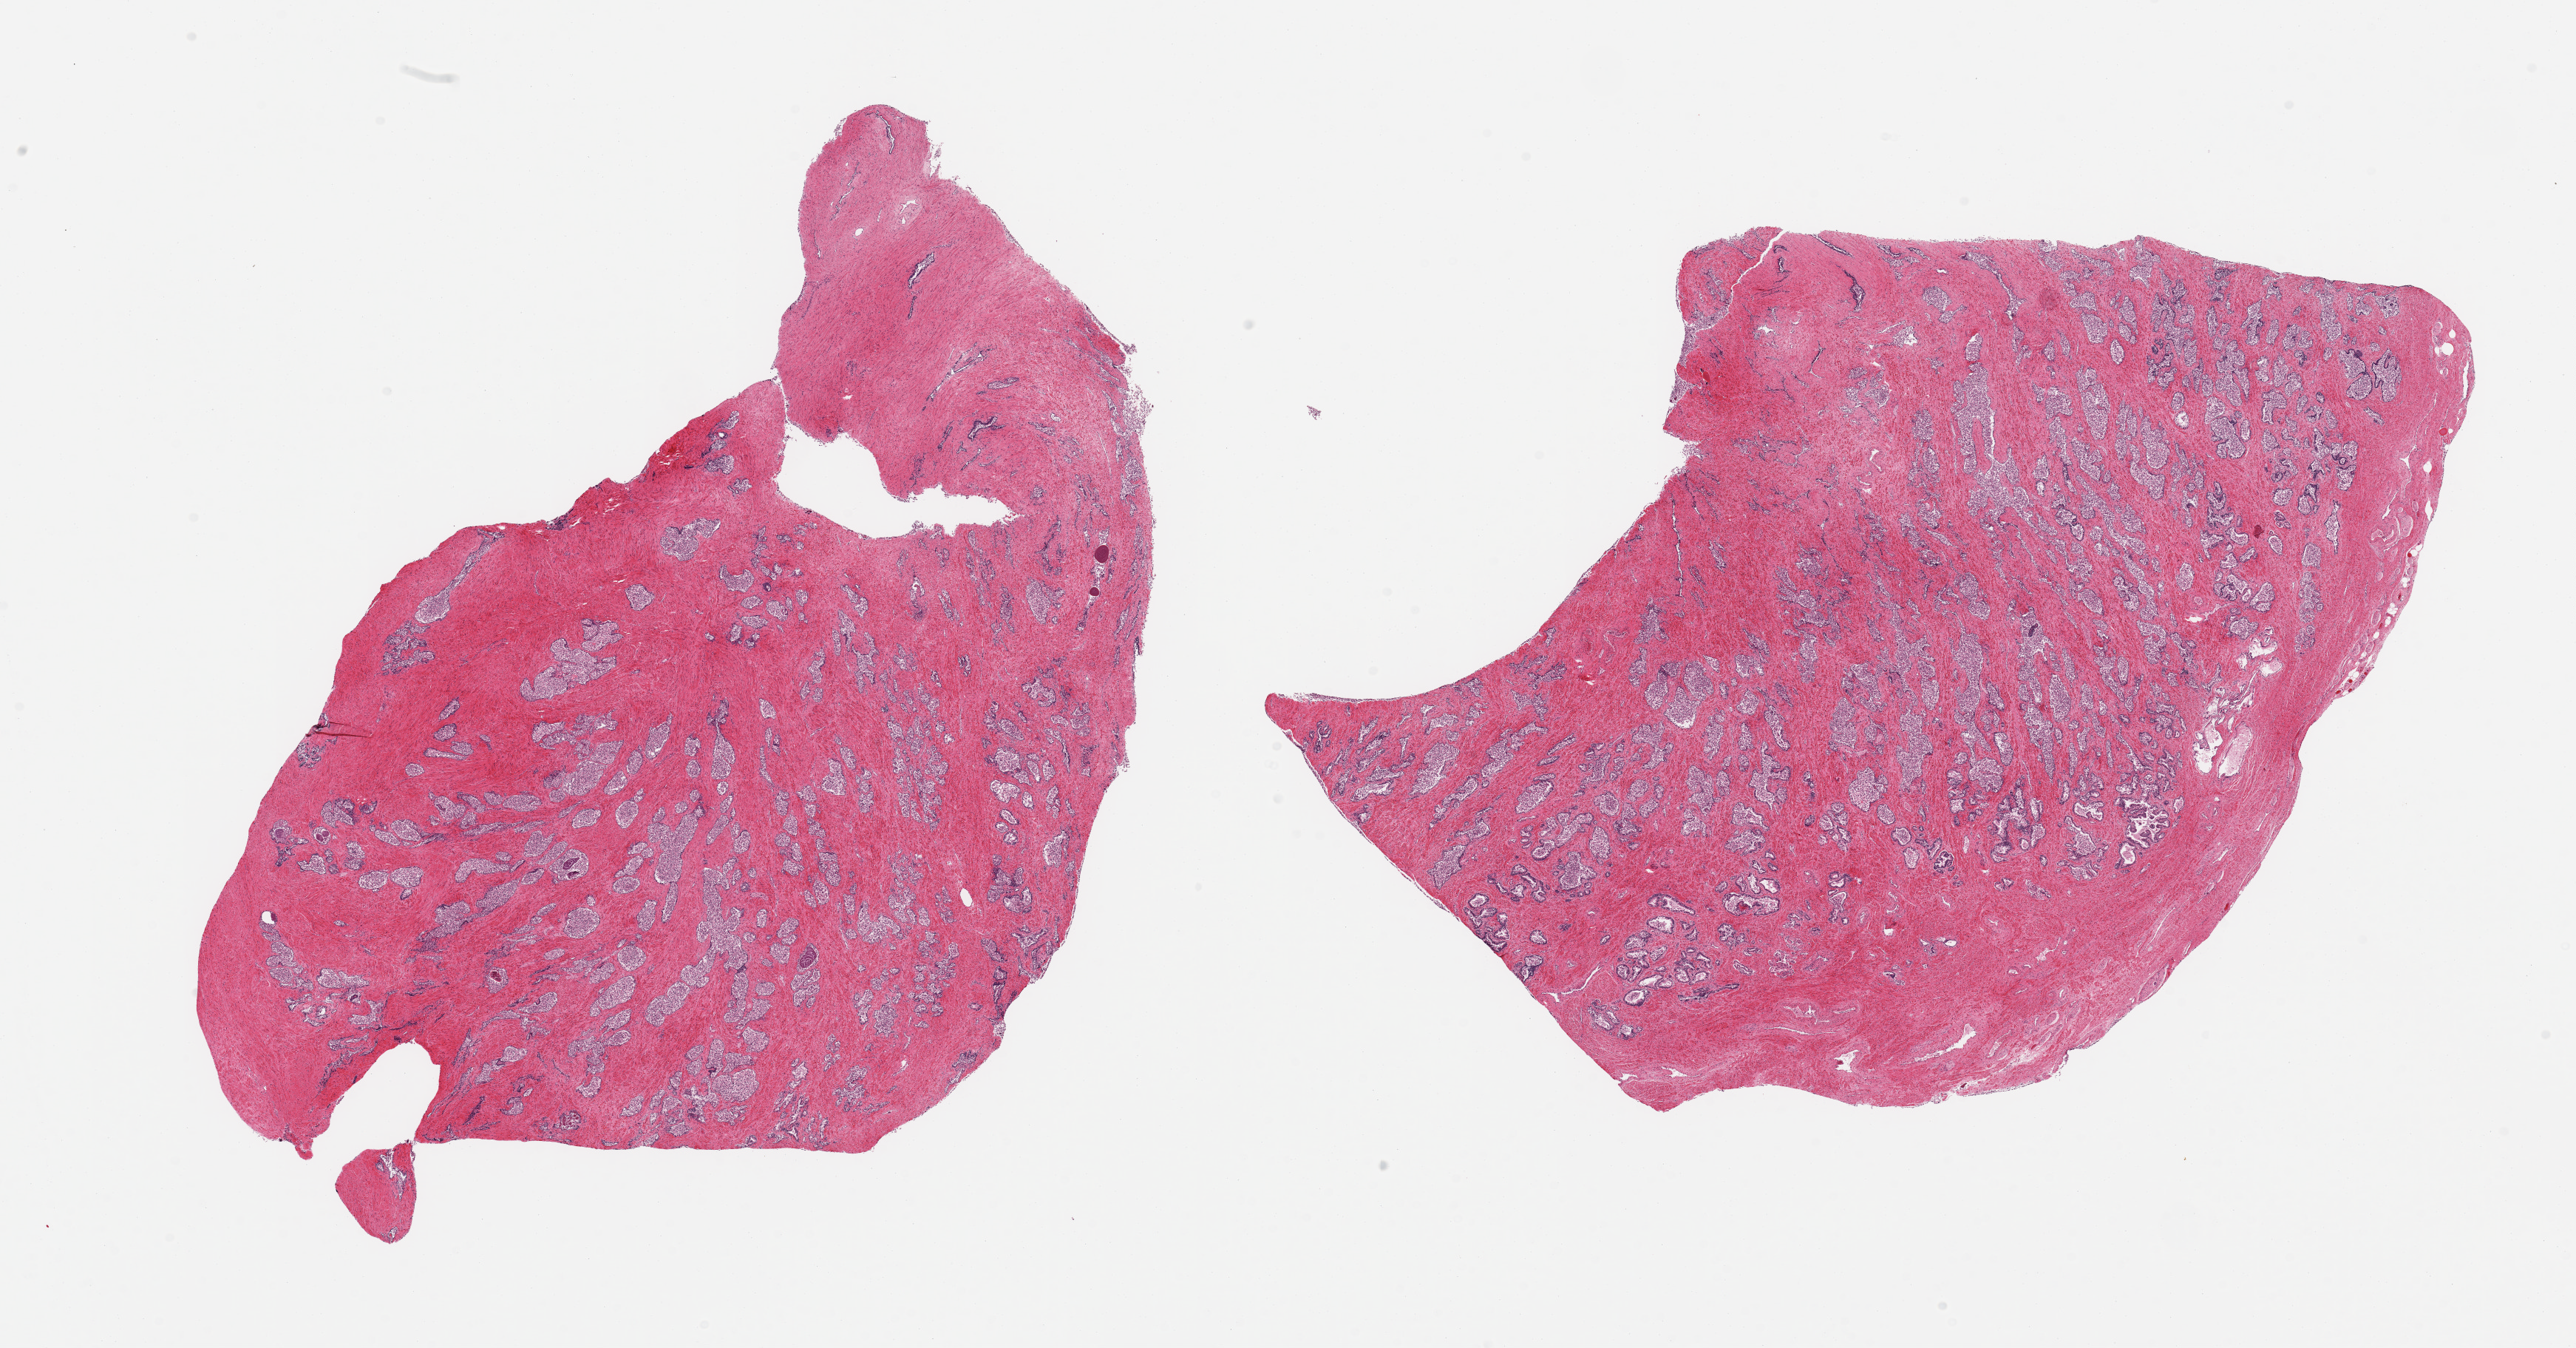
Haematoxylin and eosin whole-slide image, low-resolution overview of the scanned area, about 27.6 x 14.4 mm (acquisition: 20x scan); PAXgene-fixed, paraffin-embedded tissue; section of prostate (target tissue); donor tissue sample. Donor: male.
Review note (as recorded): 2 pieces; mild to moderate autolysis; well preserved fibromuscular stroma and glandular component with diffusely sloughed lining epithelium.